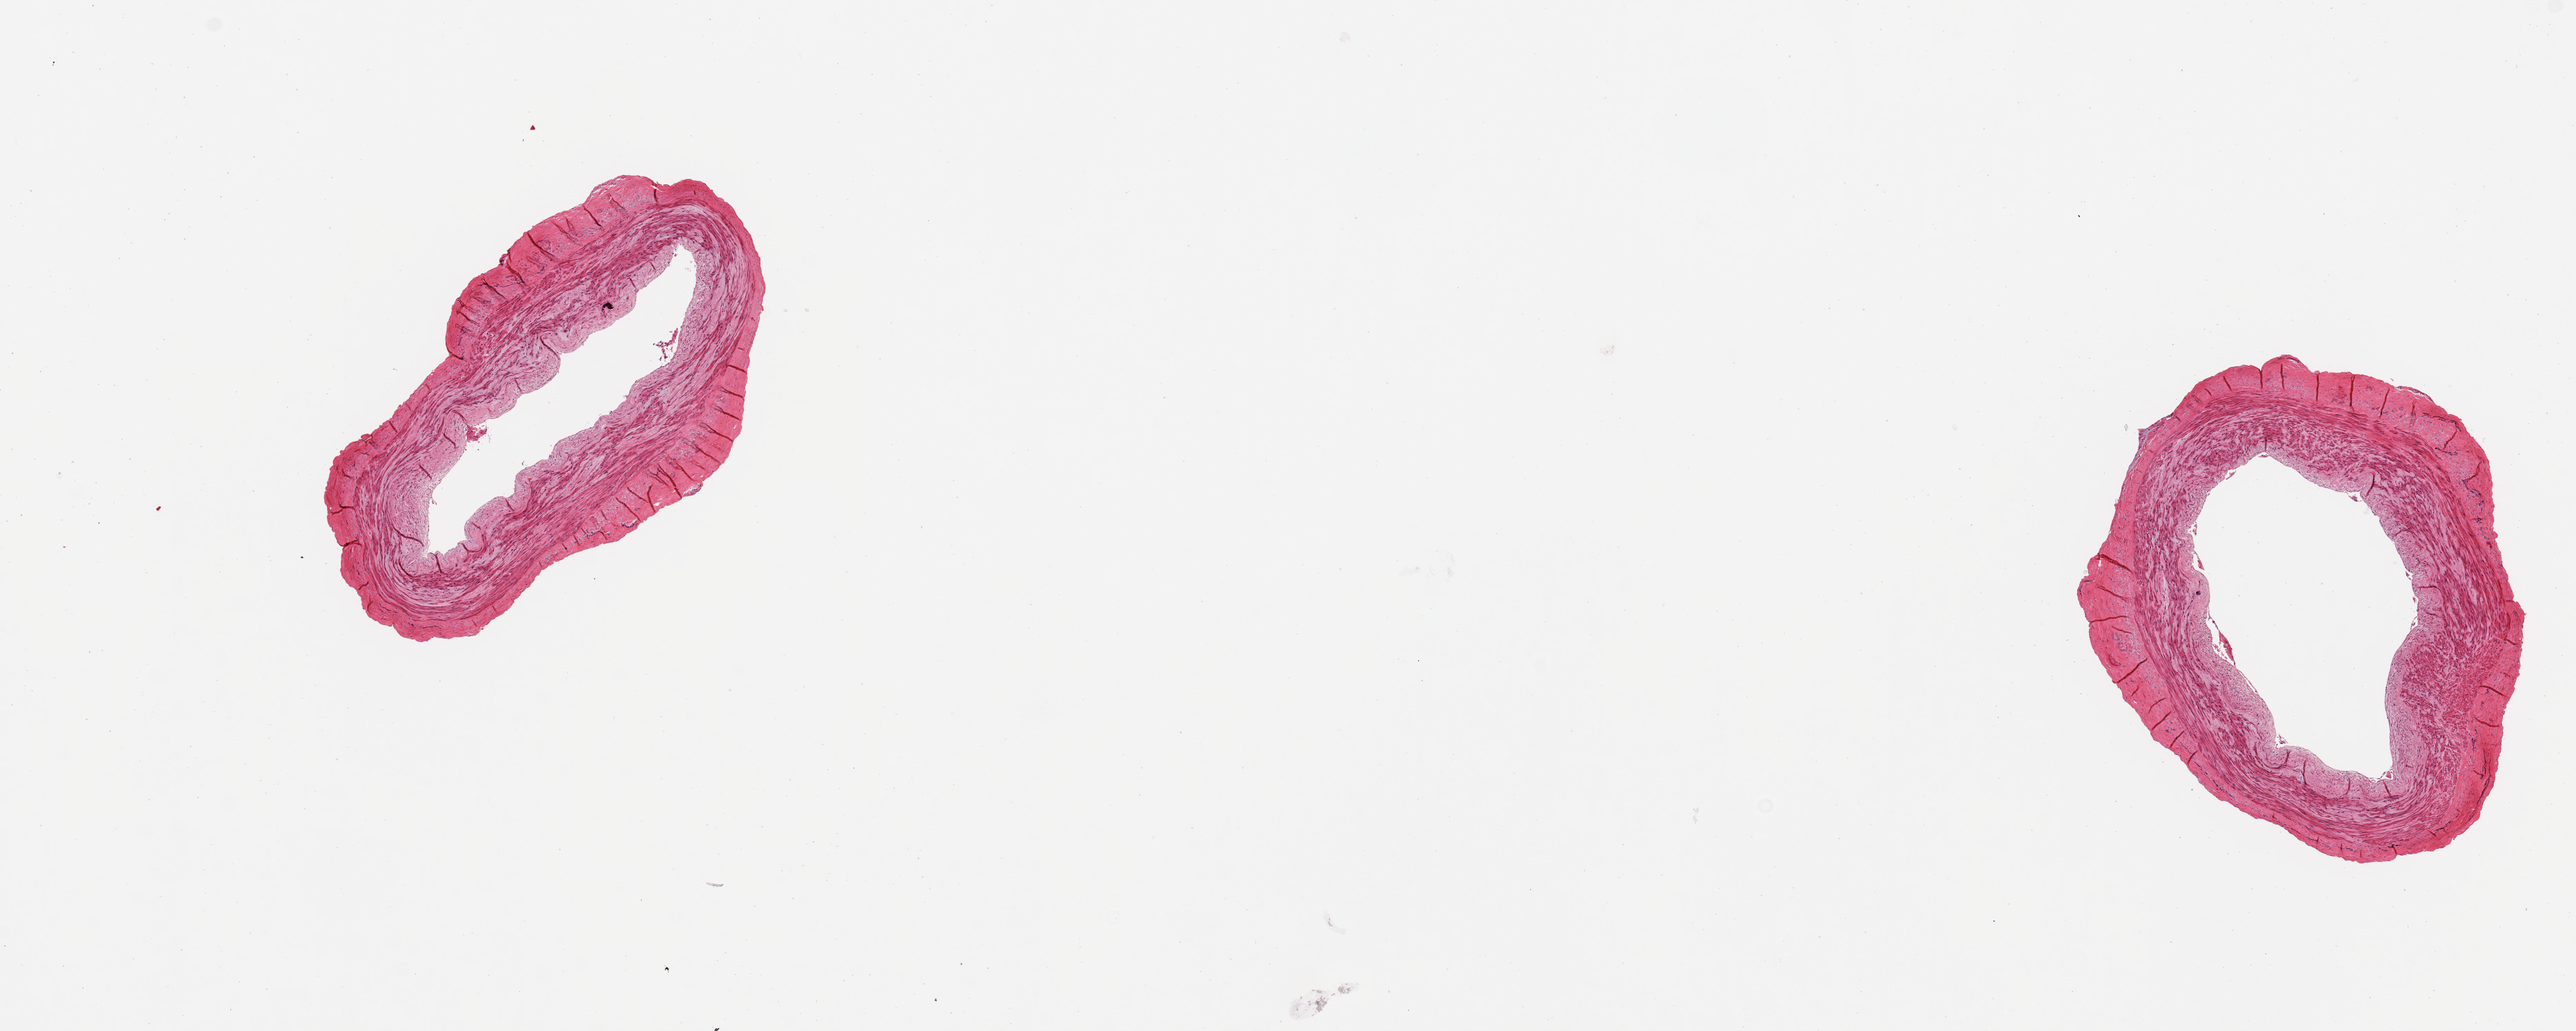
H&E whole-slide image — whole scanned area (about 14.8 x 5.9 mm, slide scanned at 20x) shown as a low-resolution overview; PAXgene-fixed, paraffin-embedded tissue; section of tibial artery (target tissue); tissue donor sample. Donor: male.
Pathologist's review note for this sample: 2 pieces, no adherent fat or significant atherosis.